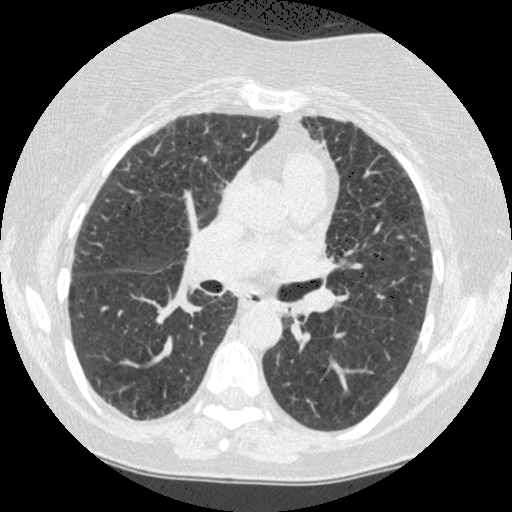
Chest CT (low-dose screening protocol), one axial image, baseline annual screen, lung window (W 1500 / L -600 HU), 1.25 mm slice thickness, 512 × 512 image matrix. Female participant, aged 60 years at enrolment. Former smoker at enrolment.
- Lesion marked by an expert reader, bounding box <273,295,312,337> (left, top, right, bottom; pixels).
- The screening reader recorded 2 non-calcified nodules or masses ≥4 mm on this exam; which of them this box marks is not recorded.
- Participant outcome: lung cancer diagnosed 794 days after this screen — small cell carcinoma, NOS, left lower lobe, undifferentiated (G4), stage IV (AJCC 6th edition), 69 mm at pathology.